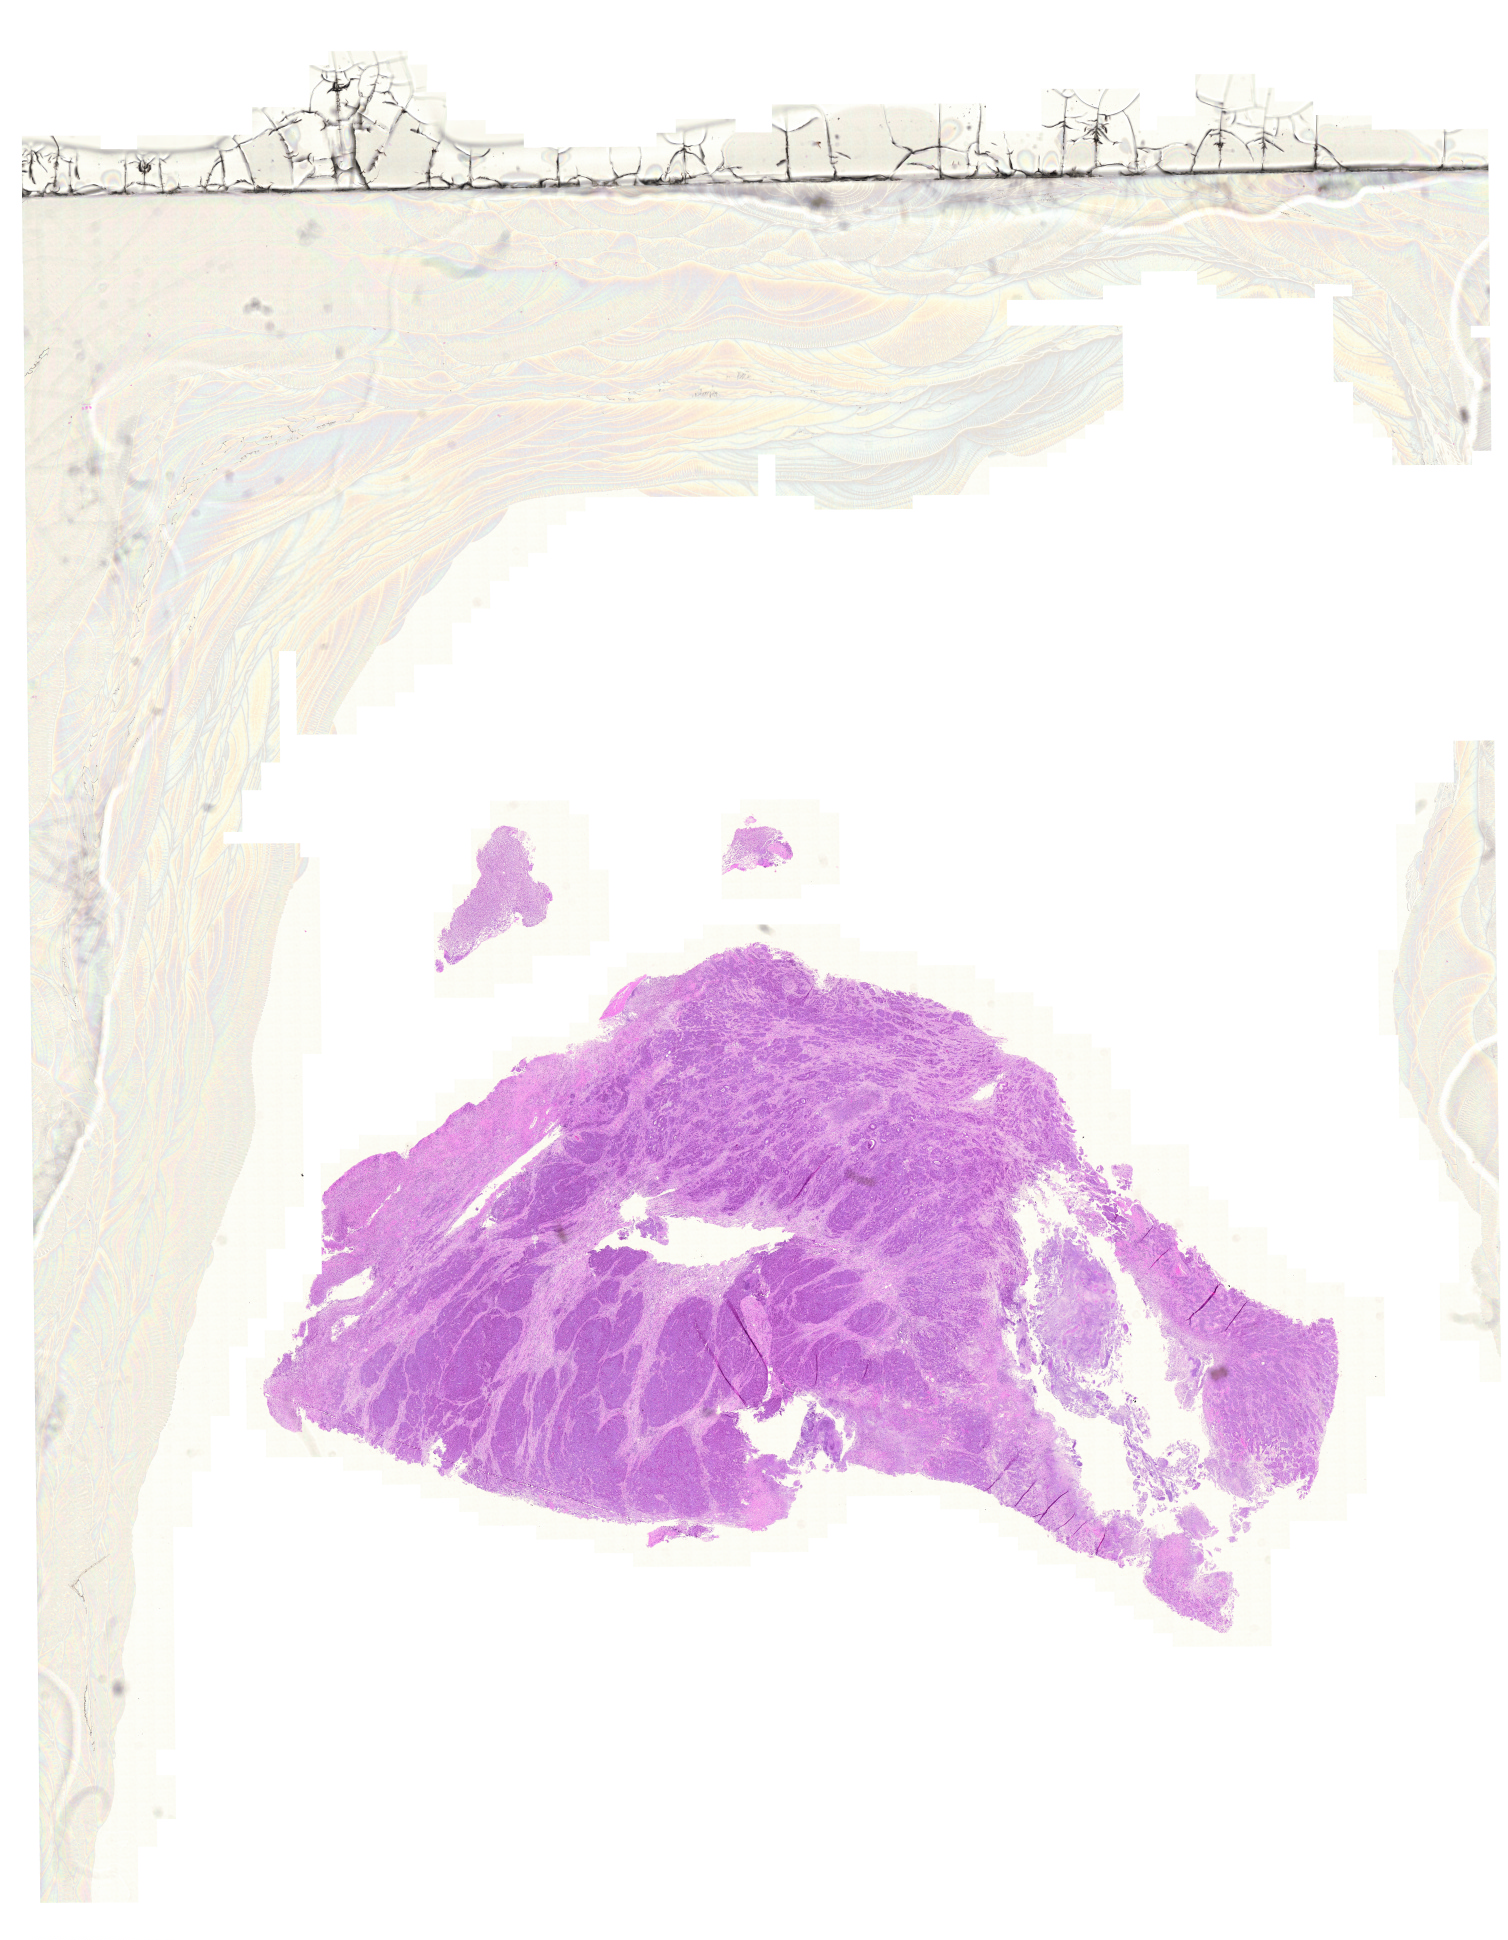
Digitized H&E-stained tissue section (whole slide), a low-resolution overview of the entire scanned area, about 22.4 x 28.9 mm (from a 20x scan); FFPE section; primary tumour sample from the colon. Female patient; age at initial diagnosis 48 years.
• TNM: T3 N0 M0
• AJCC pathologic stage: II
• pathologic diagnosis: Adenocarcinoma, NOS (ascending colon)